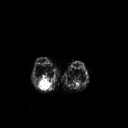
FDG PET of an extremity soft-tissue mass (from a PET/CT study), one axial slice. Position 167 of 267 along the scan axis. 128 × 128 image matrix, field of view 500 × 500 mm. Patient: female, 62 years. From the clinical record (not read from this slice): histological type: liposarcoma; site of the primary tumour: right thigh.
Outlined on this slice (expert contour drawn on MRI and transferred to this co-registered scan by the dataset authors):
- gross tumour volume (mass): bounding box [x1, y1, x2, y2] px = [38, 78, 51, 90]